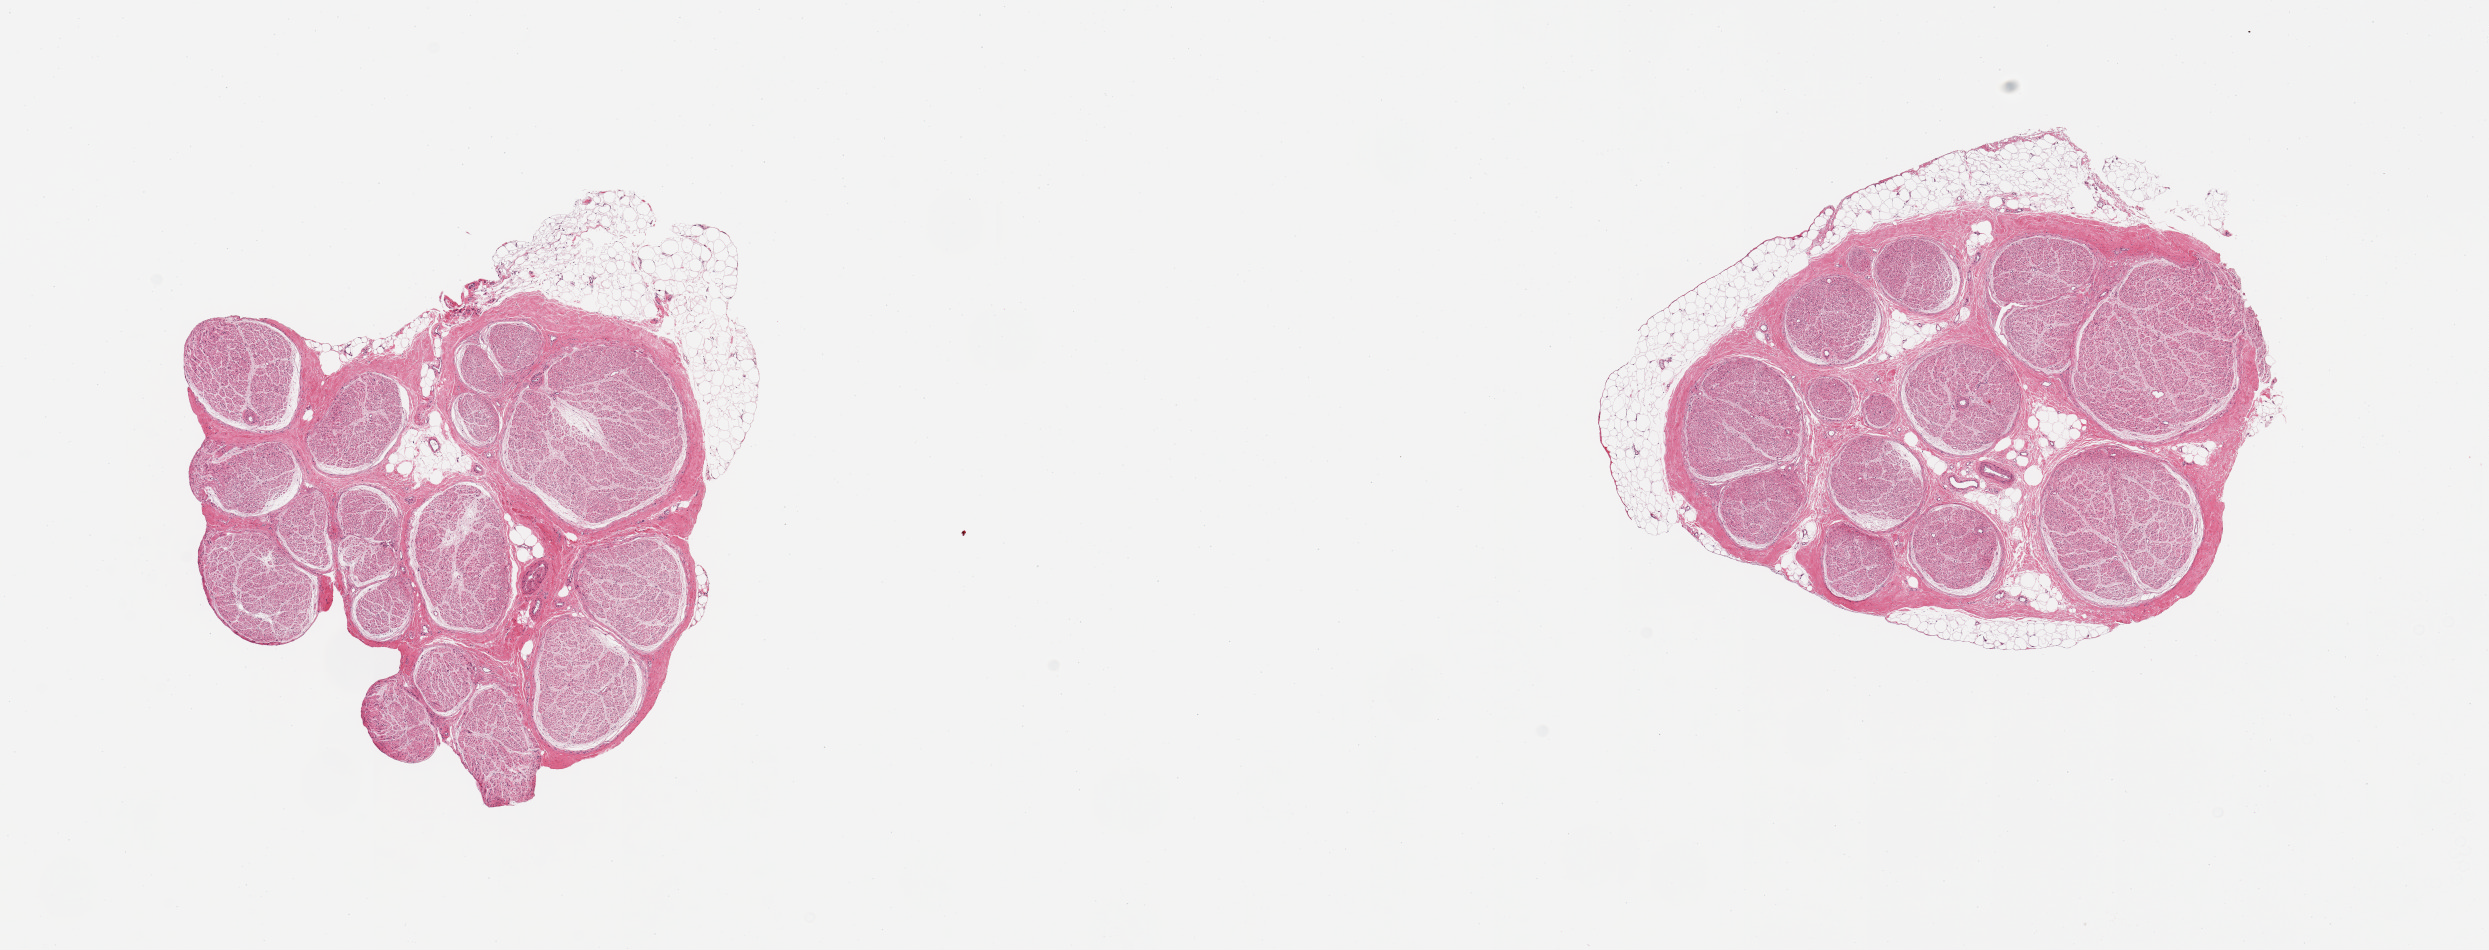
Whole-slide image, H&E stain, whole scanned area (about 19.7 x 7.5 mm) shown as a low-resolution overview. PAXgene-fixed, paraffin-embedded tissue. Target tissue: tibial nerve. Tissue donor sample. Male donor.
Review note (as recorded): 2 pieces, adherent rims of fat, up to ~0.8mm.